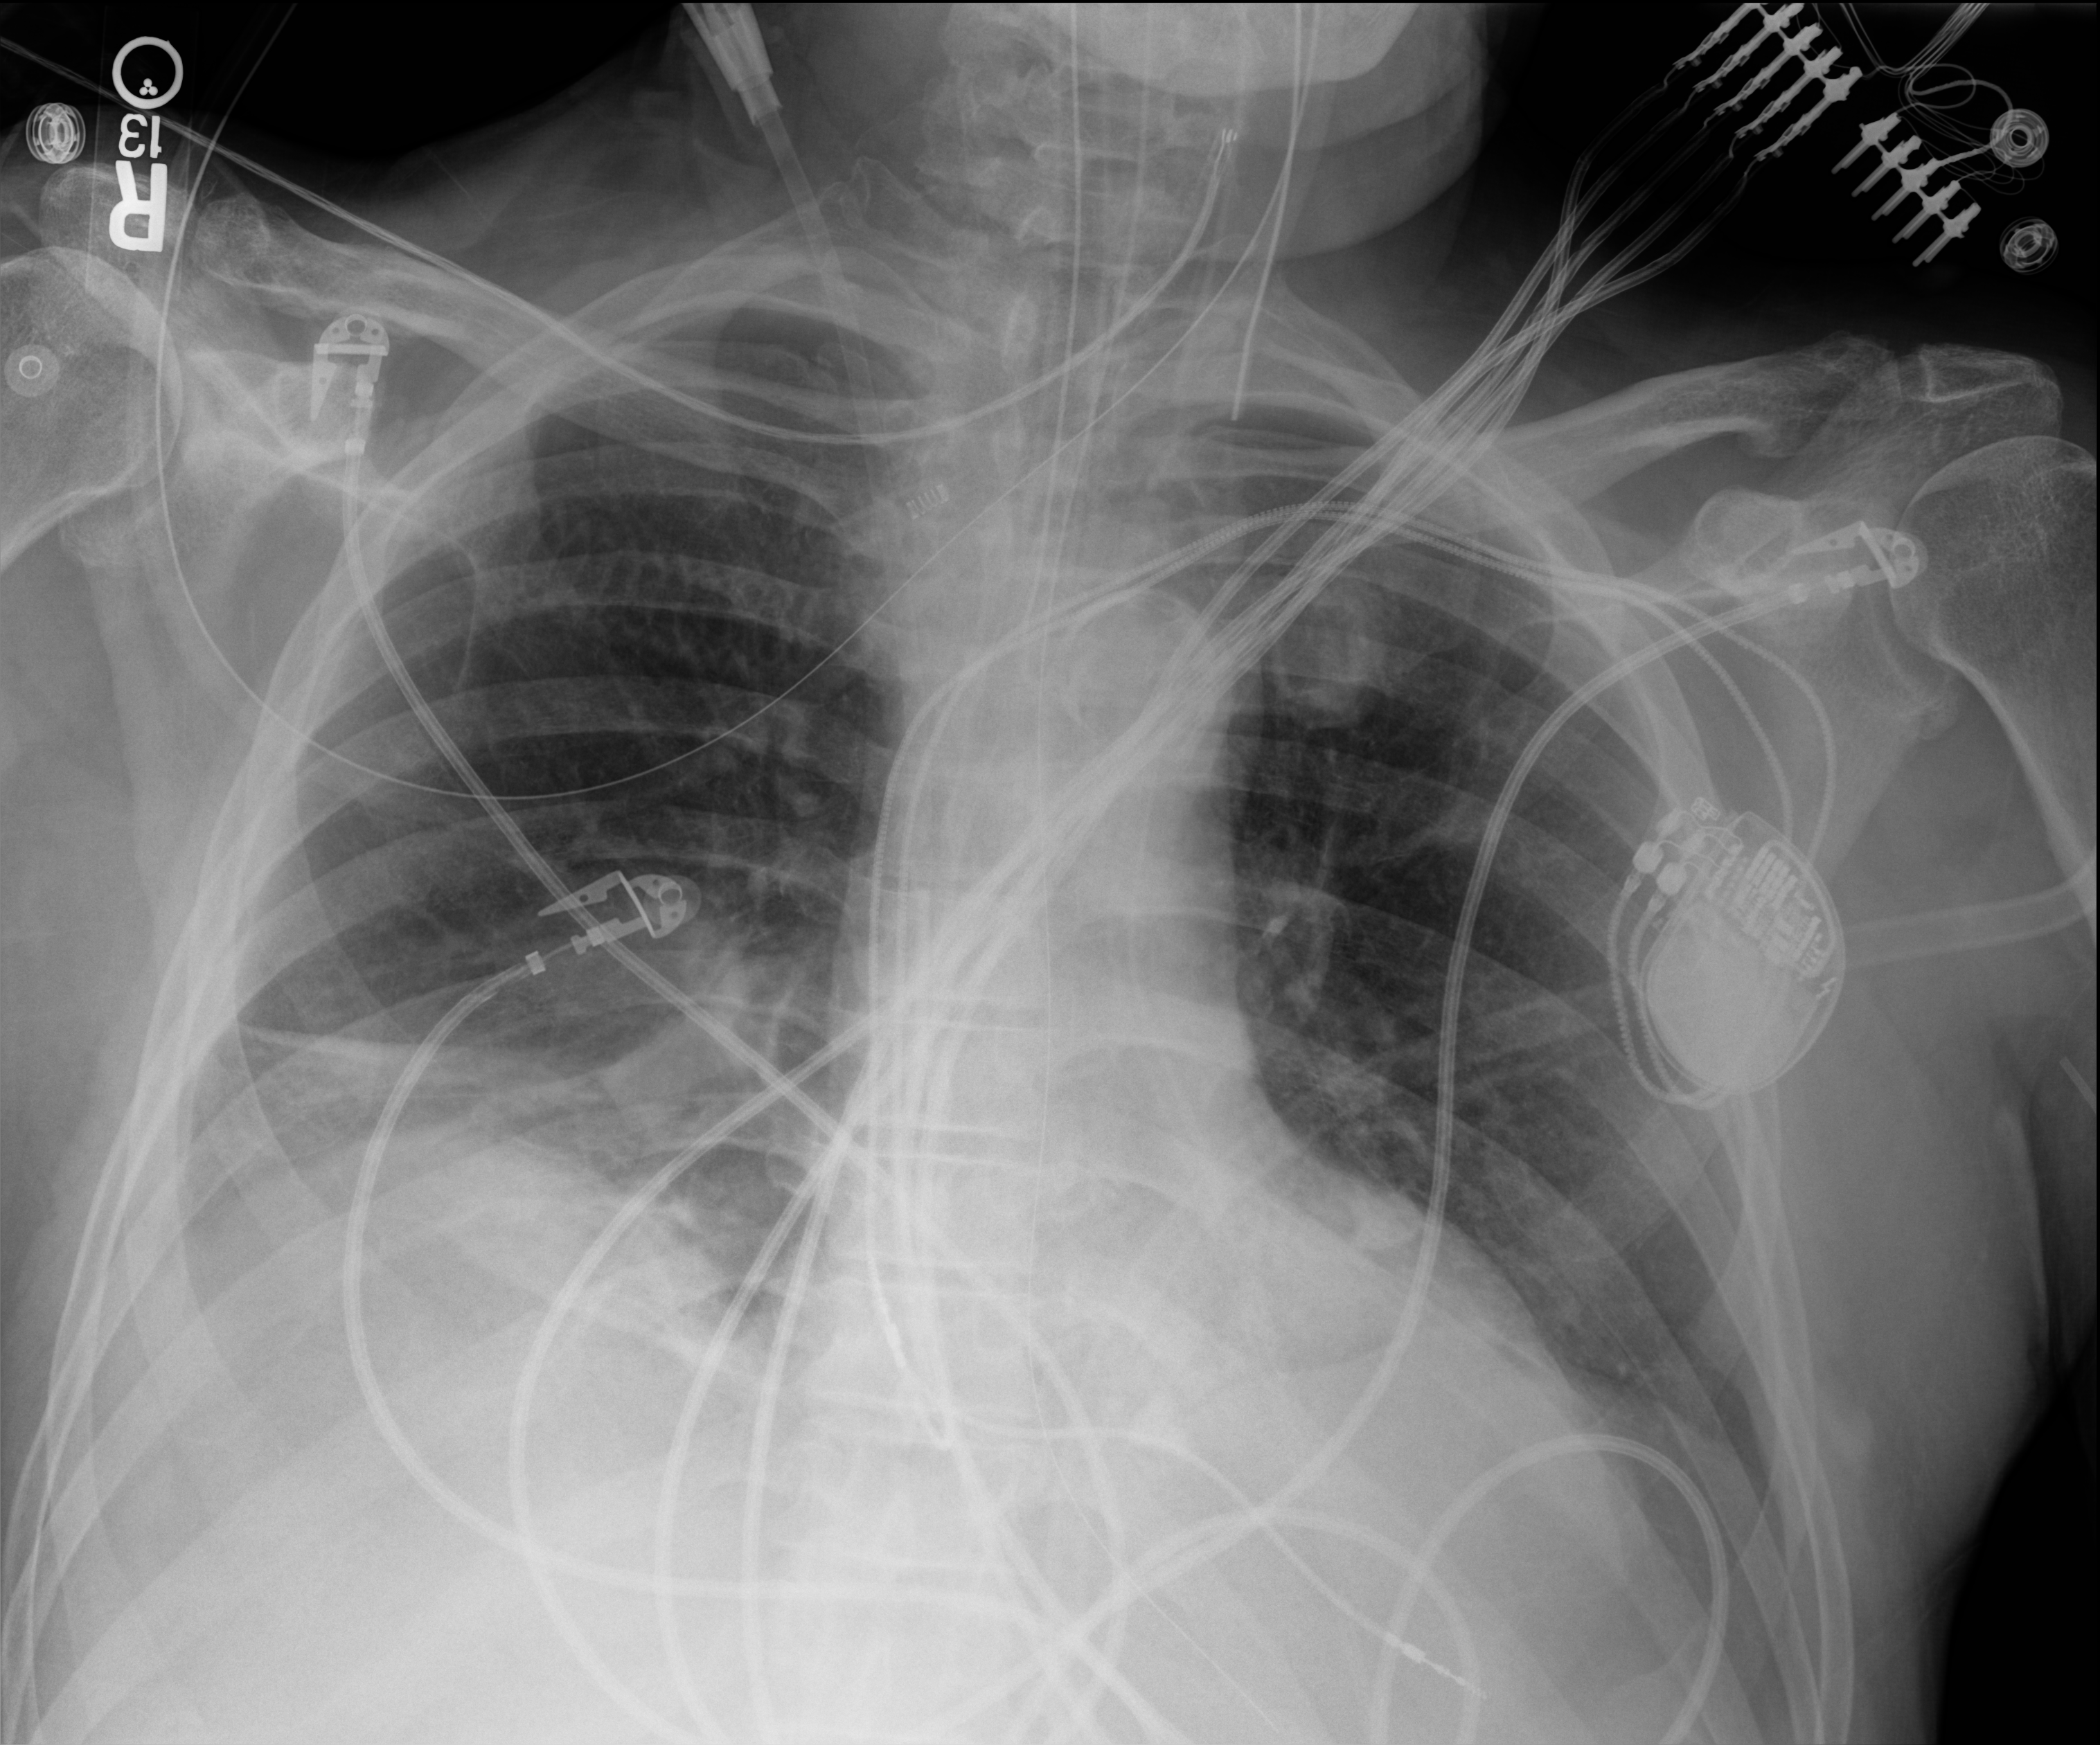
Chest X-ray (portable), anteroposterior (AP) projection. Patient hospitalised with COVID-19; male, aged 60–74 years.
Hospital-stay facts (about this admission, not read from this image; timing relative to this image not recorded): mechanically ventilated during this hospital stay: yes.